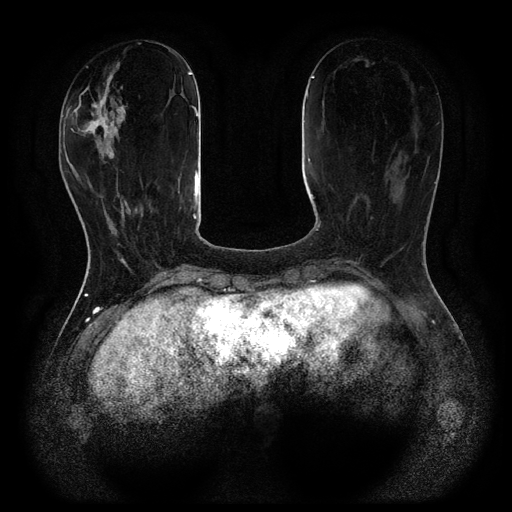
Breast MRI (dynamic contrast-enhanced, multi-phase), one axial slice; slice 32 of 116 in the series (ordered by position); dynamic contrast-enhanced series, time point 2 of 5 at this slice position (early post-contrast); 1.5 T; TE 2.6 ms, TR 5.4 ms; 512 × 512 image matrix, field of view 340 × 340 mm. Female patient, age 48 years.
Outlined on this slice (semi-automatically segmented with operator editing):
- breast lesion (labelled benign in the annotation): bounding box <74,60,129,160> (left, top, right, bottom; pixels)